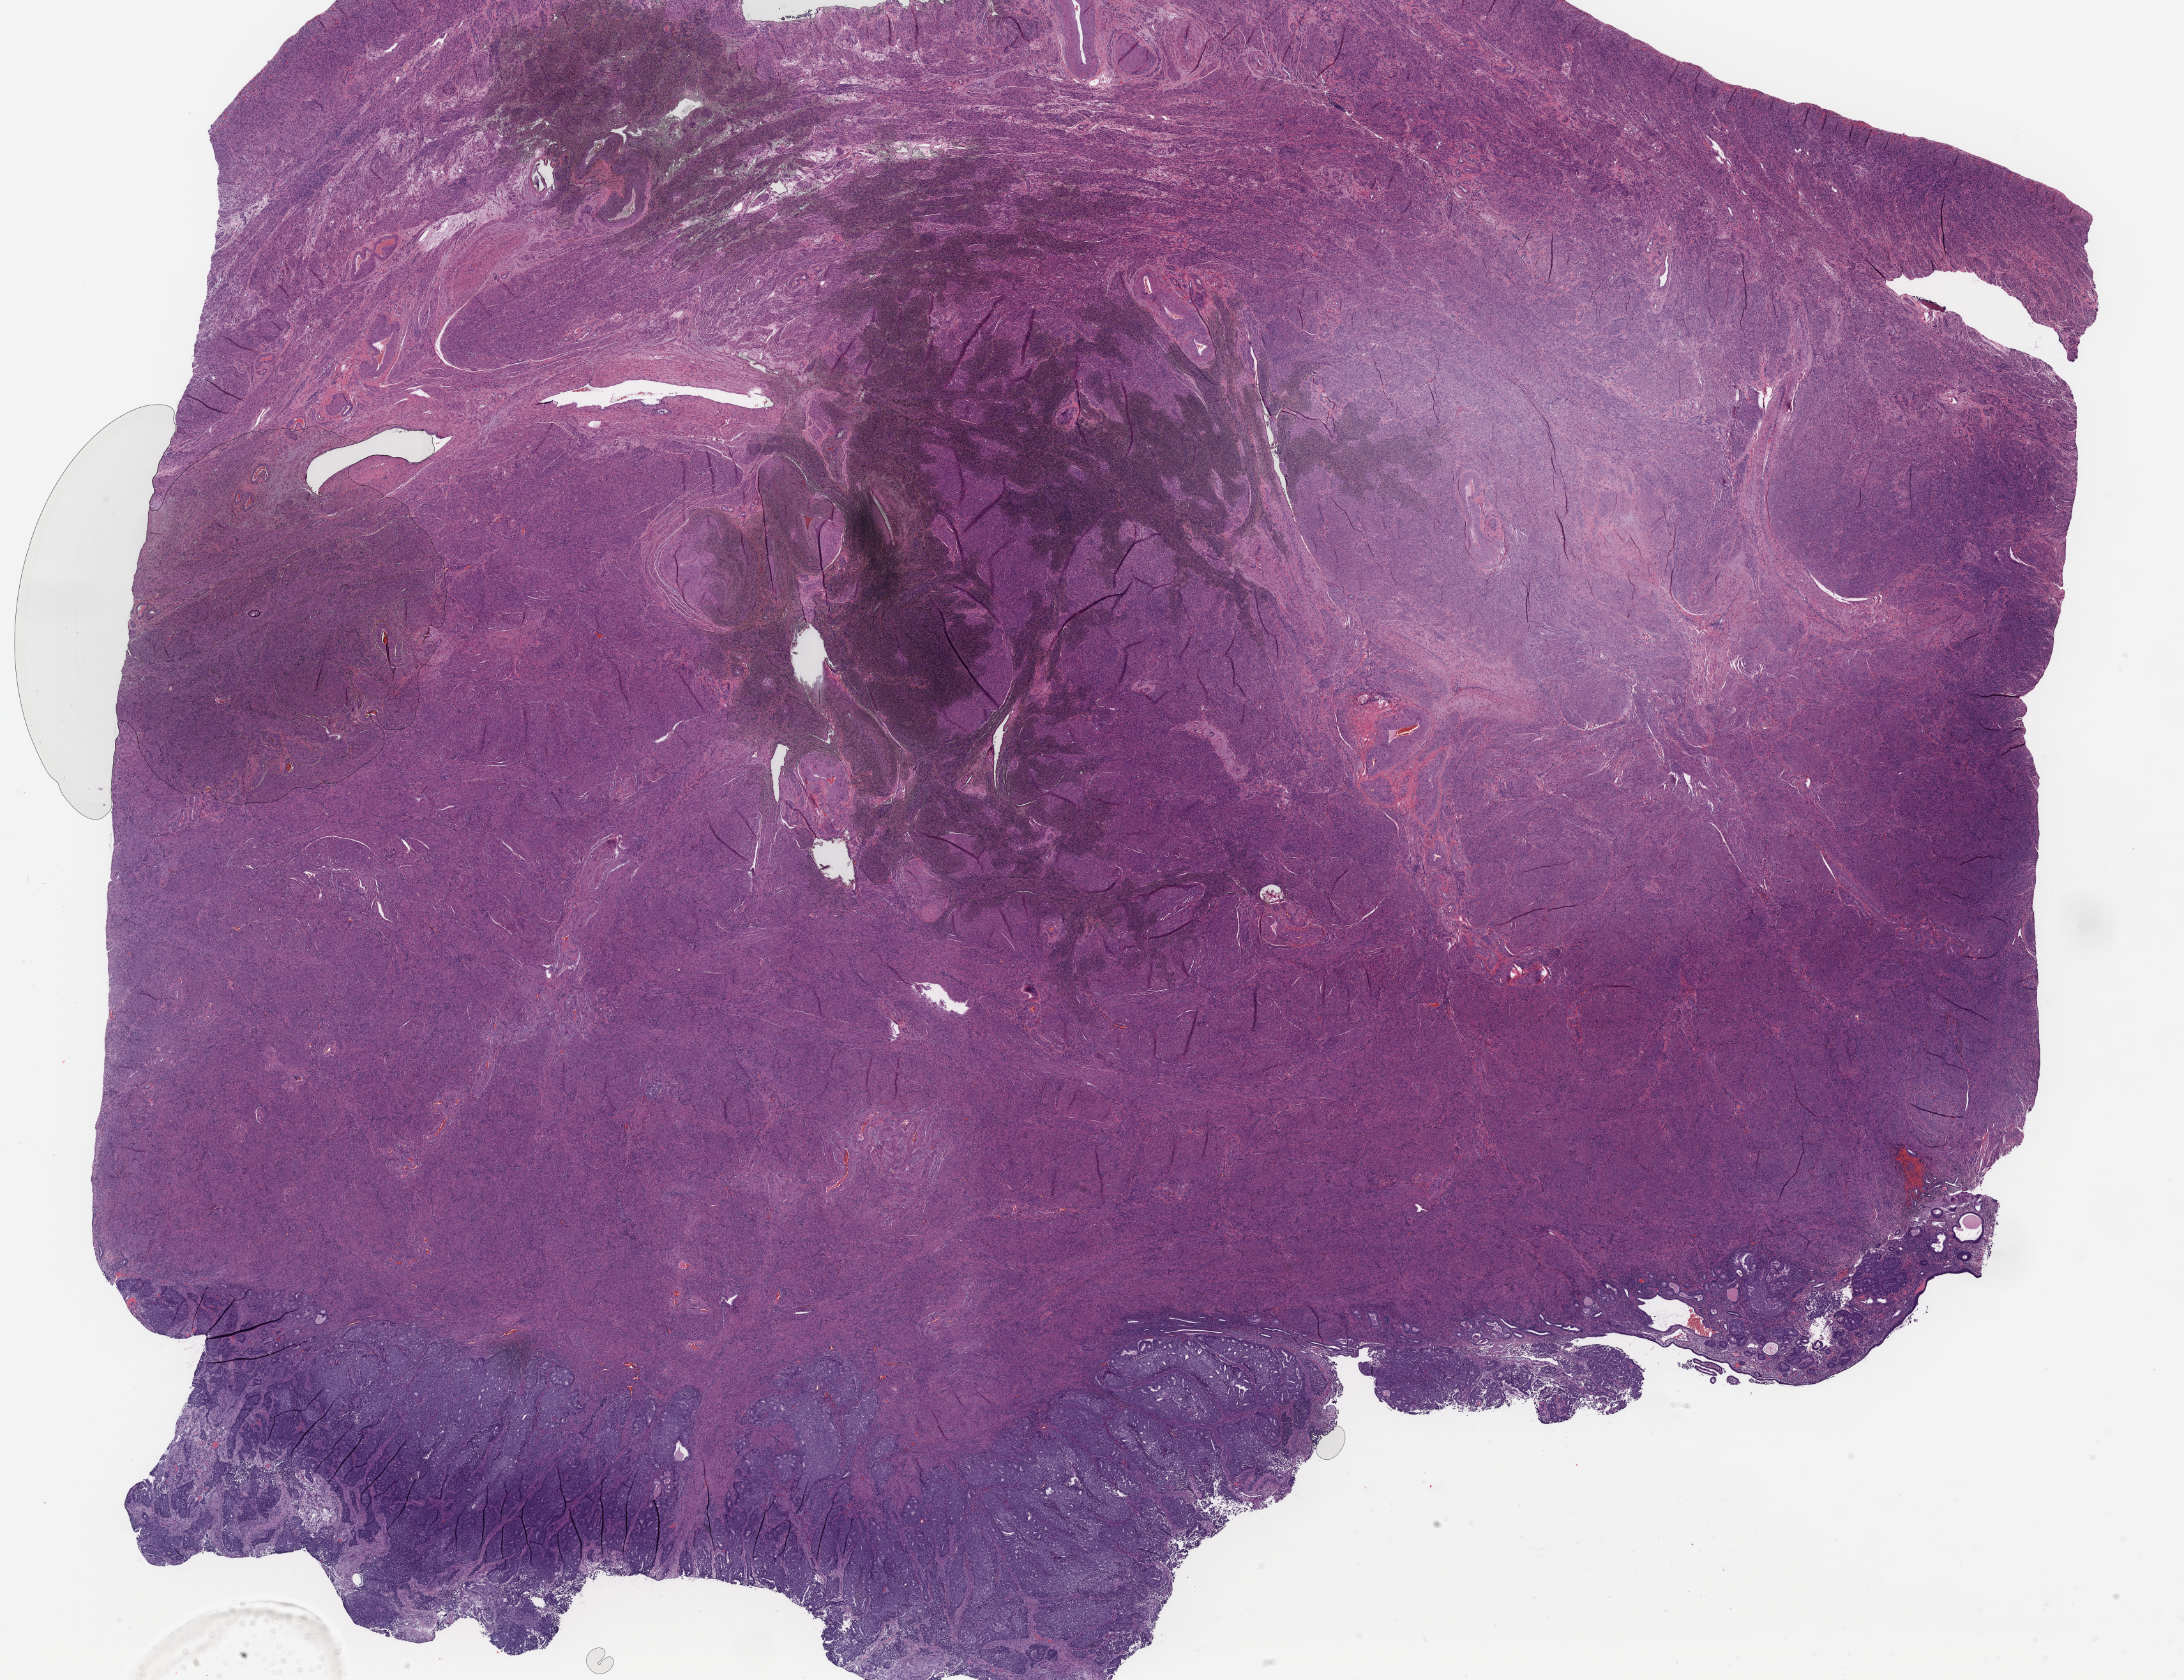
Hematoxylin and eosin (H&E) stained whole-slide image — low-resolution overview of the scanned area, about 27.0 x 20.8 mm (from a 40x scan), formalin-fixed paraffin-embedded (FFPE) diagnostic section, uterus, primary tumour sample. Female, age 62 years at initial diagnosis. Histologic grade: G3 (poorly differentiated).
• pathologic diagnosis: Endometrioid adenocarcinoma, NOS (endometrium)
• FIGO stage: III